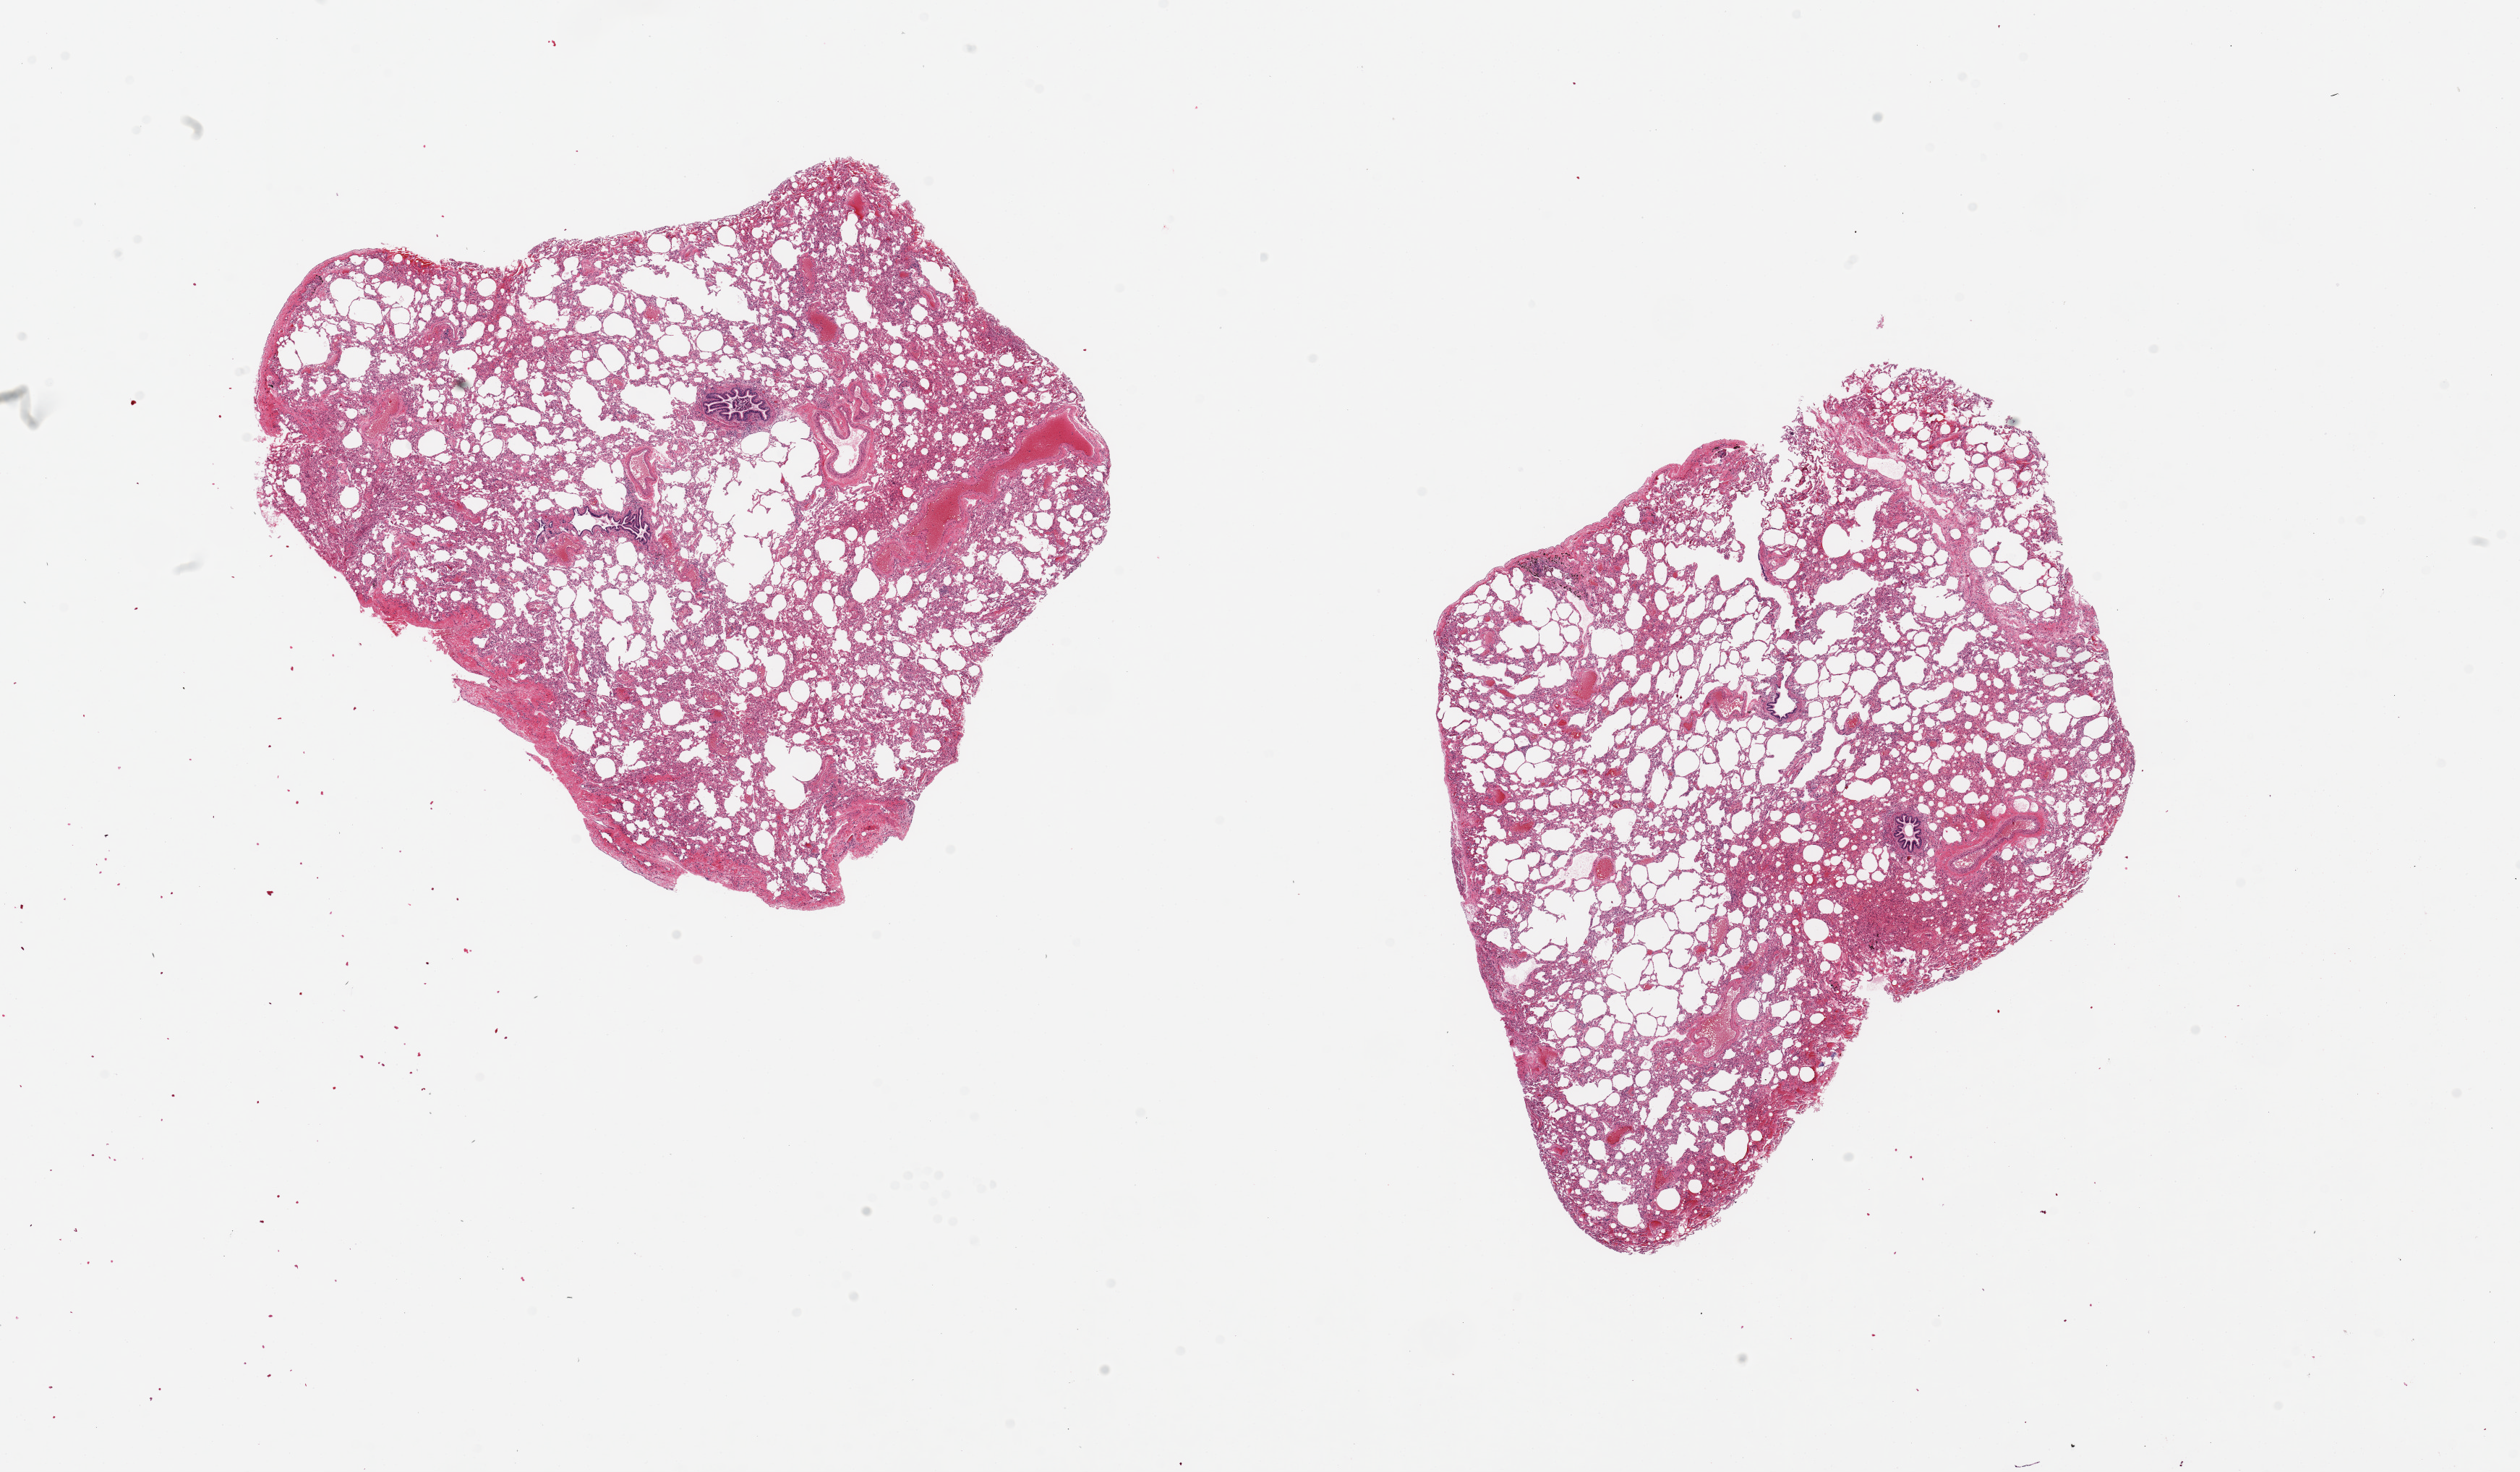
Whole-slide image, haematoxylin and eosin stain, brightfield, whole scanned area (about 27.6 x 16.1 mm) shown as a low-resolution overview. PAXgene-fixed, paraffin-embedded tissue. Target tissue: lung. Donor tissue sample. Donor sex: male.
* reviewer comment on this tissue sample: 2 pieces, 9x7 & 8x8mm; mild congestion; bronchioles well visualized, fairly well preserved